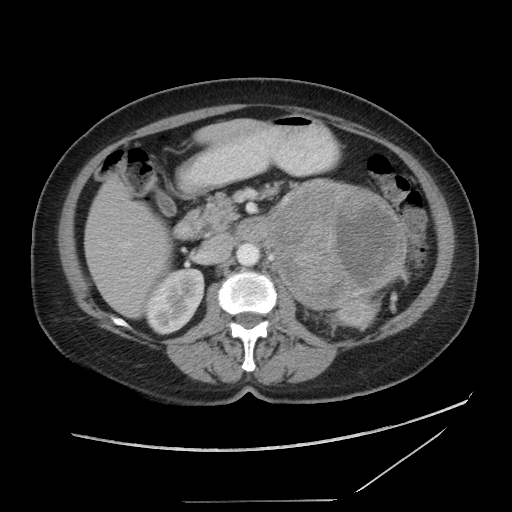
Contrast-enhanced abdominal CT, one axial slice; slice 51 of 86 in the series (ordered by position); reconstruction kernel STANDARD; 120 kVp; soft-tissue window (W 400 / L 40 HU); 5 mm slice thickness; 512 × 512 image matrix. Patient: female, 77 years. Case-level facts recorded for this patient, not image findings: diagnosis: adrenocortical carcinoma; tumour side: left adrenal; tumour size at pathology: 13.1 cm; Ki-67 index: 10 %.
Annotated regions visible in this slice (semi-automatic segmentation, software-assisted and operator-edited):
- mass: bounding box [x1, y1, x2, y2] px = [267, 180, 406, 308]